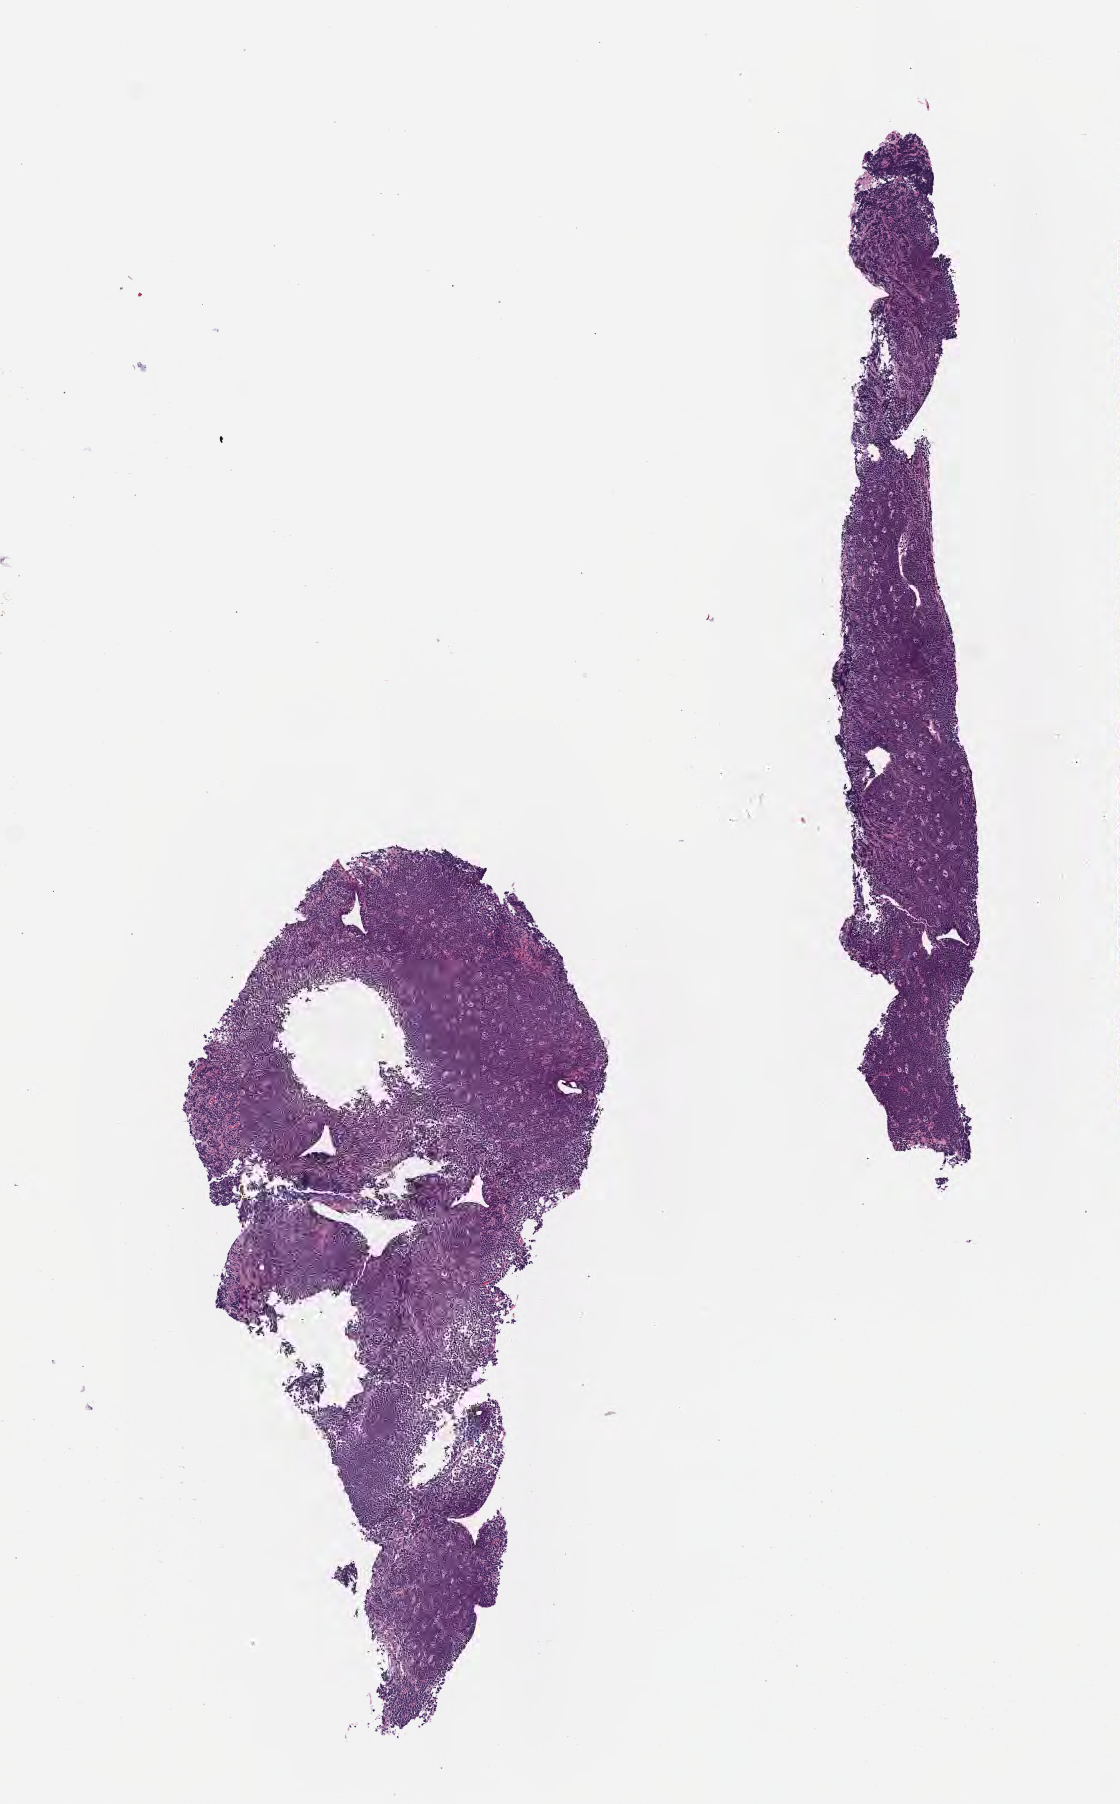
Whole-slide image, hematoxylin and eosin (H&E) stain, shown as a low-resolution overview of the whole scanned area (about 4.5 x 7.3 mm), formalin-fixed paraffin-embedded section, specimen: primary tumor. Male patient; age at initial diagnosis 8 years. Composition of this section per pathologist review: tumor cells 95%, tumor nuclei 95%, stromal cells 0%, necrosis 5%, normal cells 0%. Infiltration values recorded for this section: lymphocyte infiltration 10%, monocyte infiltration 30%, neutrophil infiltration 10%.
* diagnosis: Burkitt lymphoma, NOS
* Ann Arbor stage (patient): Stage IV
* section: top of the tissue portion